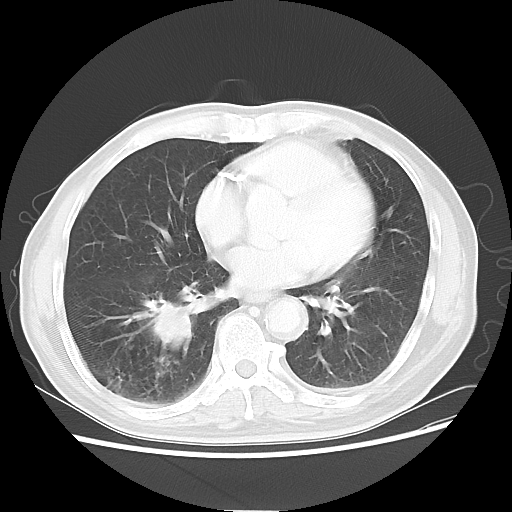
Chest CT, one axial slice; slice 24 of 58 in the series (ordered by position); reconstruction kernel LUNG; 120 kVp; lung window (W 1500 / L -600 HU); 5 mm slice thickness; 512 × 512 image matrix, field of view 360 × 360 mm. Patient: male, 74 years. From the clinical record (not read from this slice): clinical TNM (as recorded): T1c N1 M1.
Annotated regions visible in this slice (bounding box drawn by a radiologist):
- lung tumour (recorded histology: adenocarcinoma): bounding box <124,293,195,361> (left, top, right, bottom; pixels)